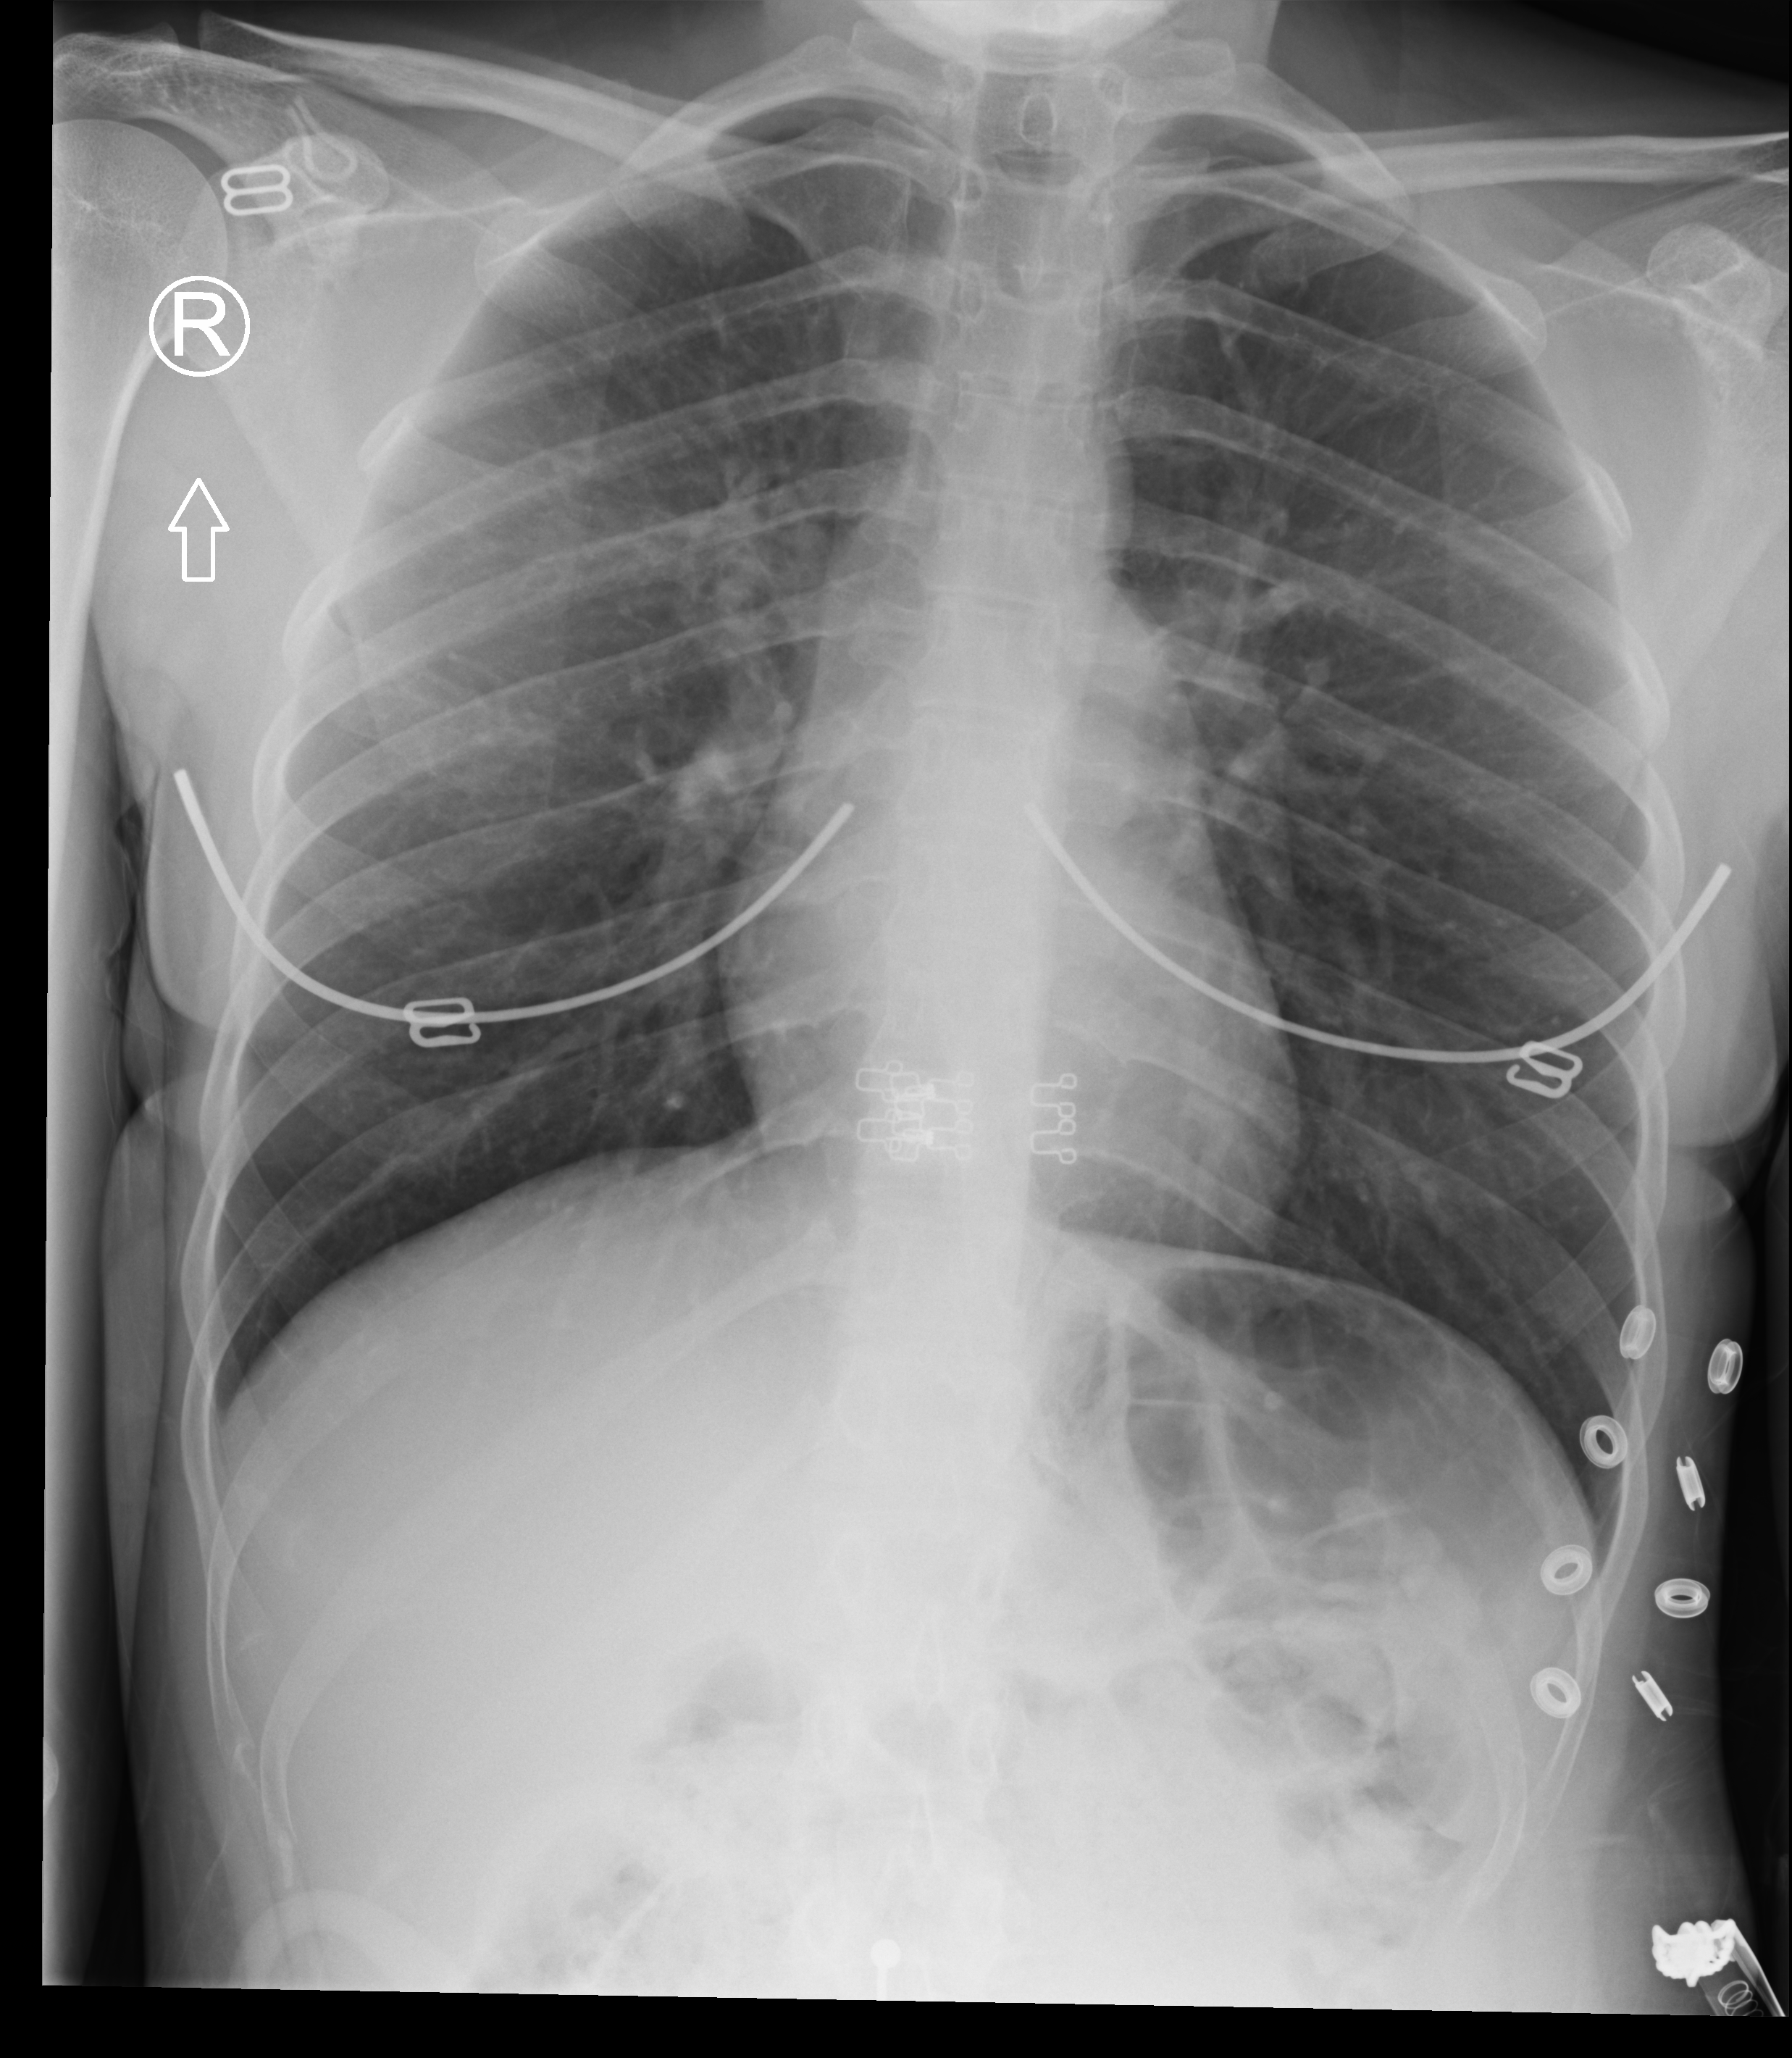
Chest X-ray (portable); anteroposterior (AP) projection. Female patient hospitalised with COVID-19, age 18–59 years.
From the hospital-stay record, not from the radiograph (when in the stay this image was taken is not recorded): mechanically ventilated during this hospital stay: no.